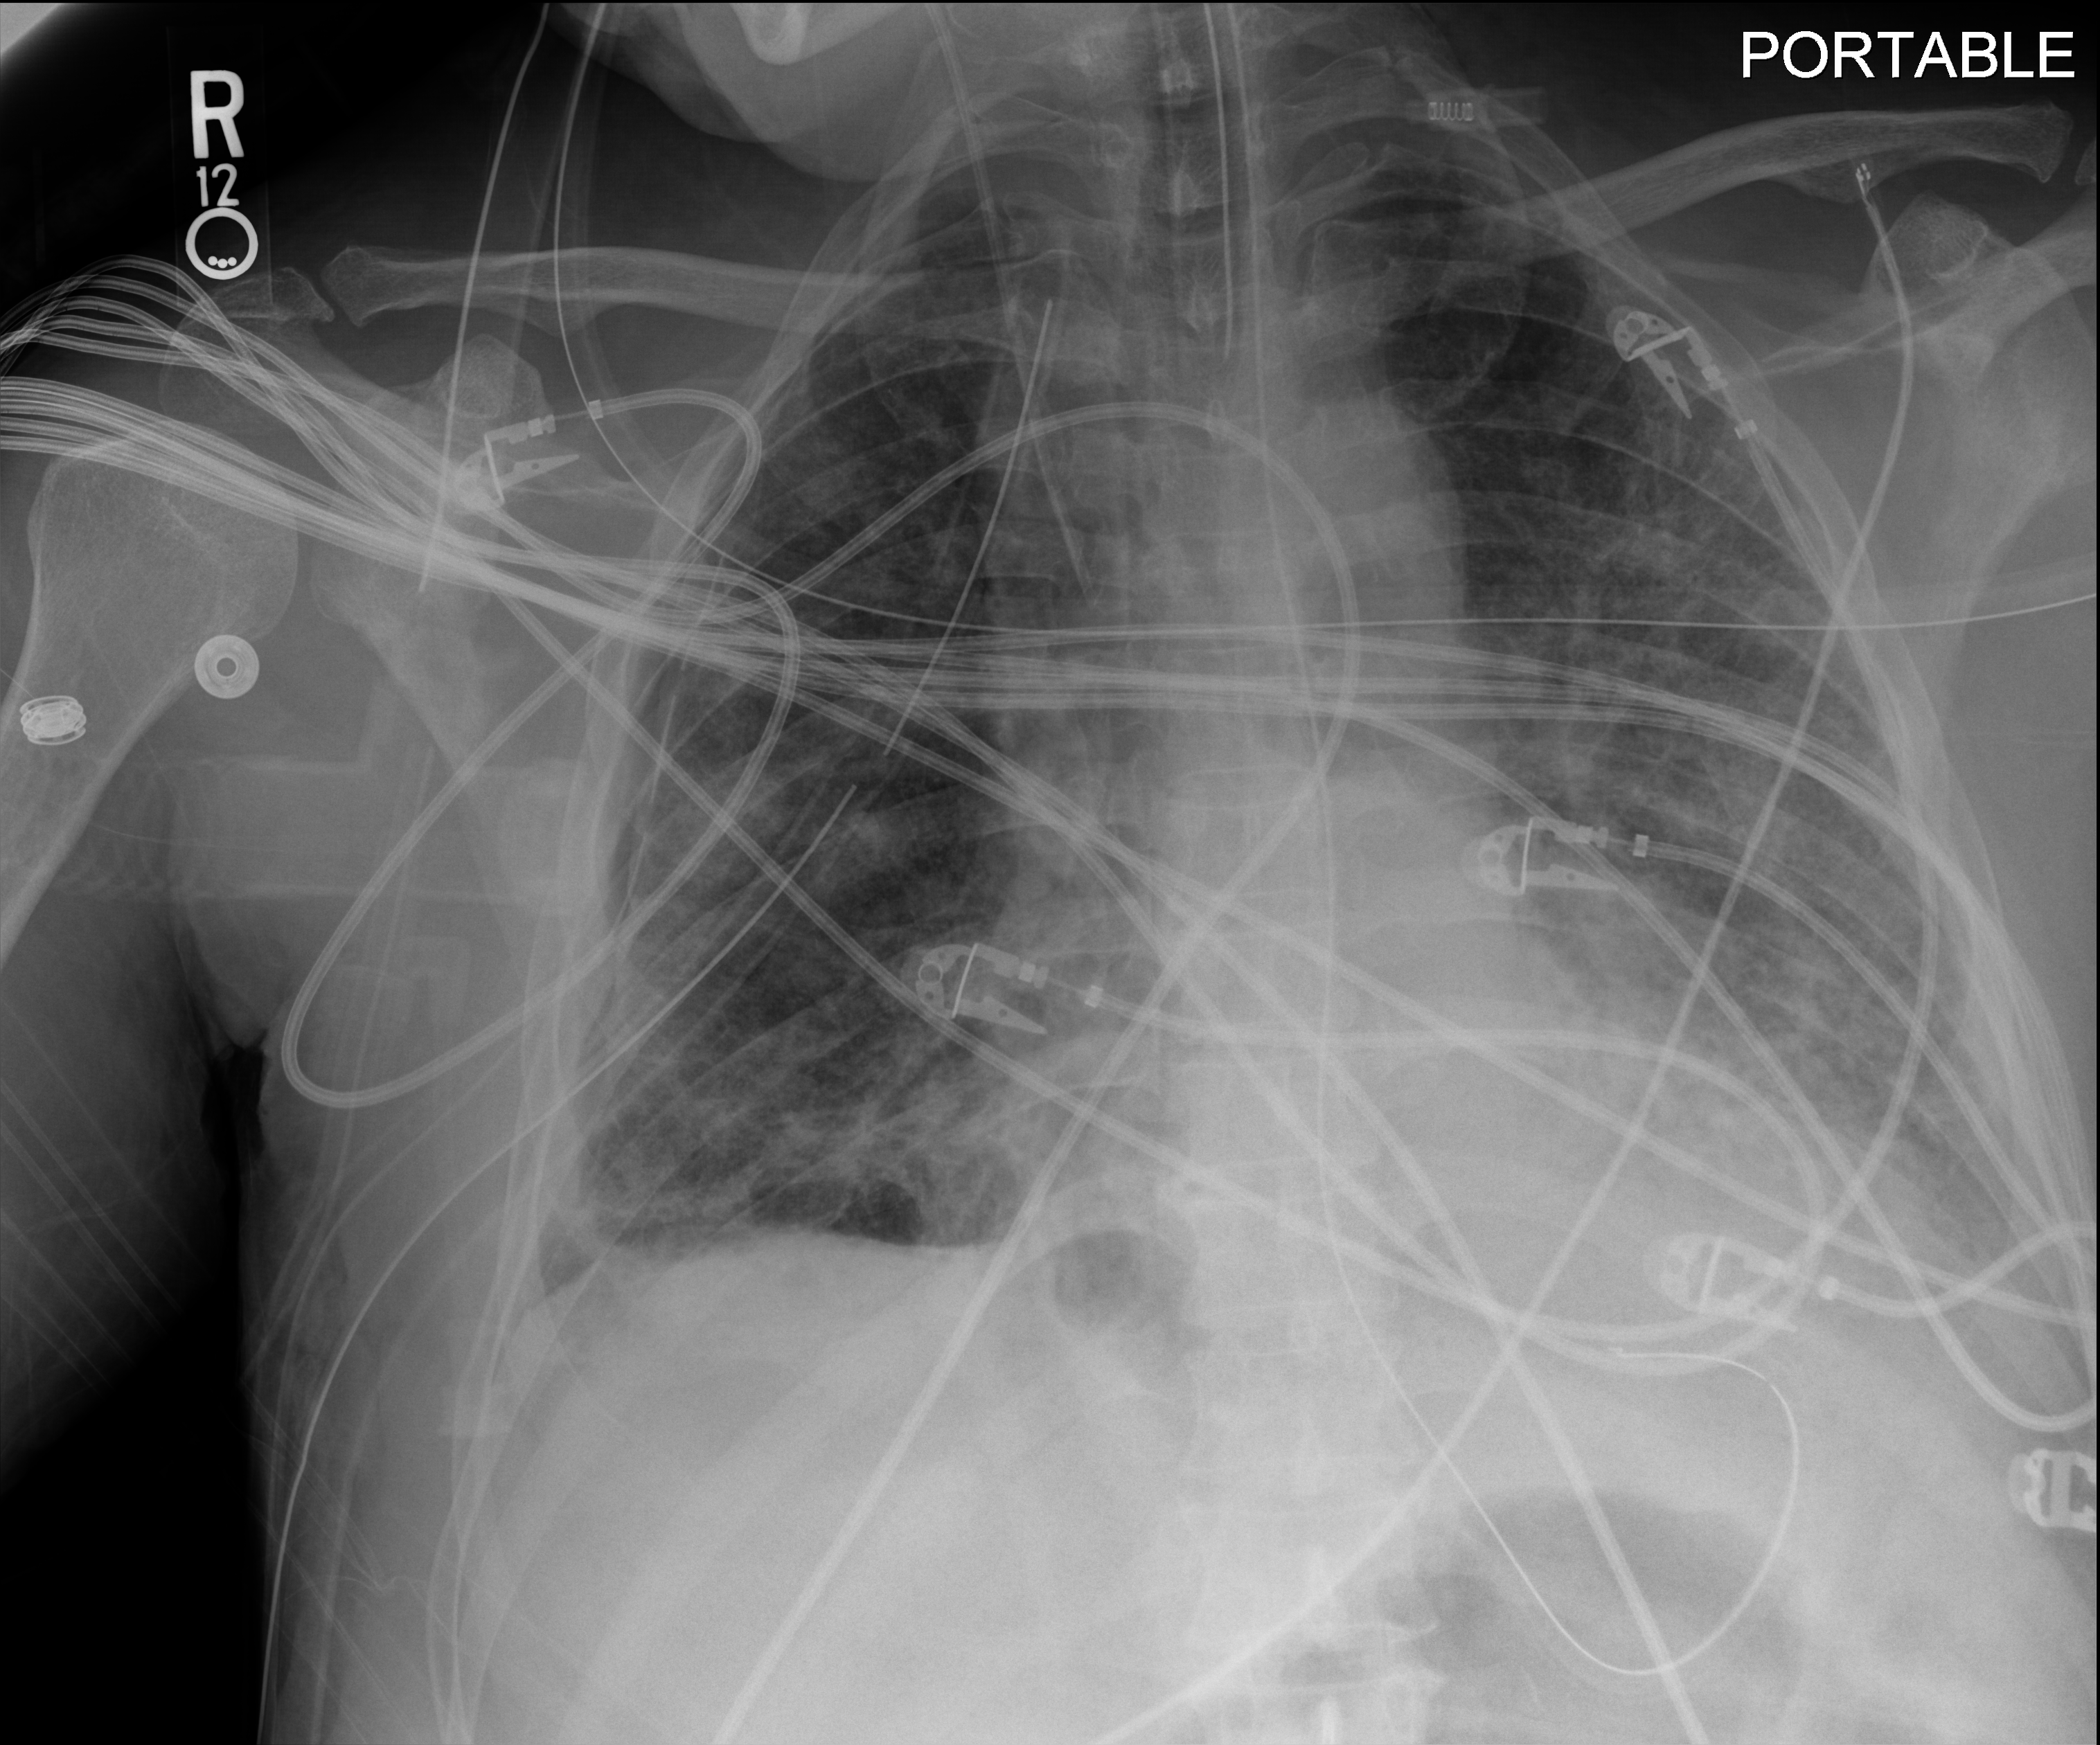
Chest X-ray (portable); anteroposterior (AP) projection. Patient hospitalised with COVID-19; male, aged 60–74 years.
From the hospital-stay record, not from the radiograph (when in the stay this image was taken is not recorded): length of hospital stay: 37 days; mechanically ventilated during this hospital stay: yes.